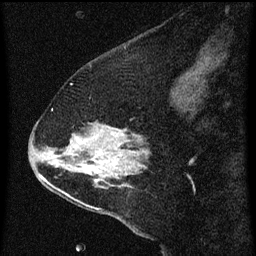
Breast MRI (dynamic contrast-enhanced), one sagittal slice. Slice 18 of 60 in the series (ordered by position). Dynamic contrast-enhanced series, image 2 of 3 at this slice position (ordered by acquisition). 1.5 T. TE 4.2 ms, TR 8 ms. 256 × 256 image matrix, field of view 180 × 180 mm. Female patient, age 47 years.
Annotated regions visible in this slice (semi-automatically segmented with operator editing):
- analysis volume of interest (the breast-tissue region the enhancement analysis was run in; not a lesion): bounding box (x1, y1, x2, y2) in pixels: (36, 108, 149, 213)
- tumour enhancement mask (voxels above the 70 % enhancement threshold inside the analysis volume of interest): (39, 130, 148, 189)